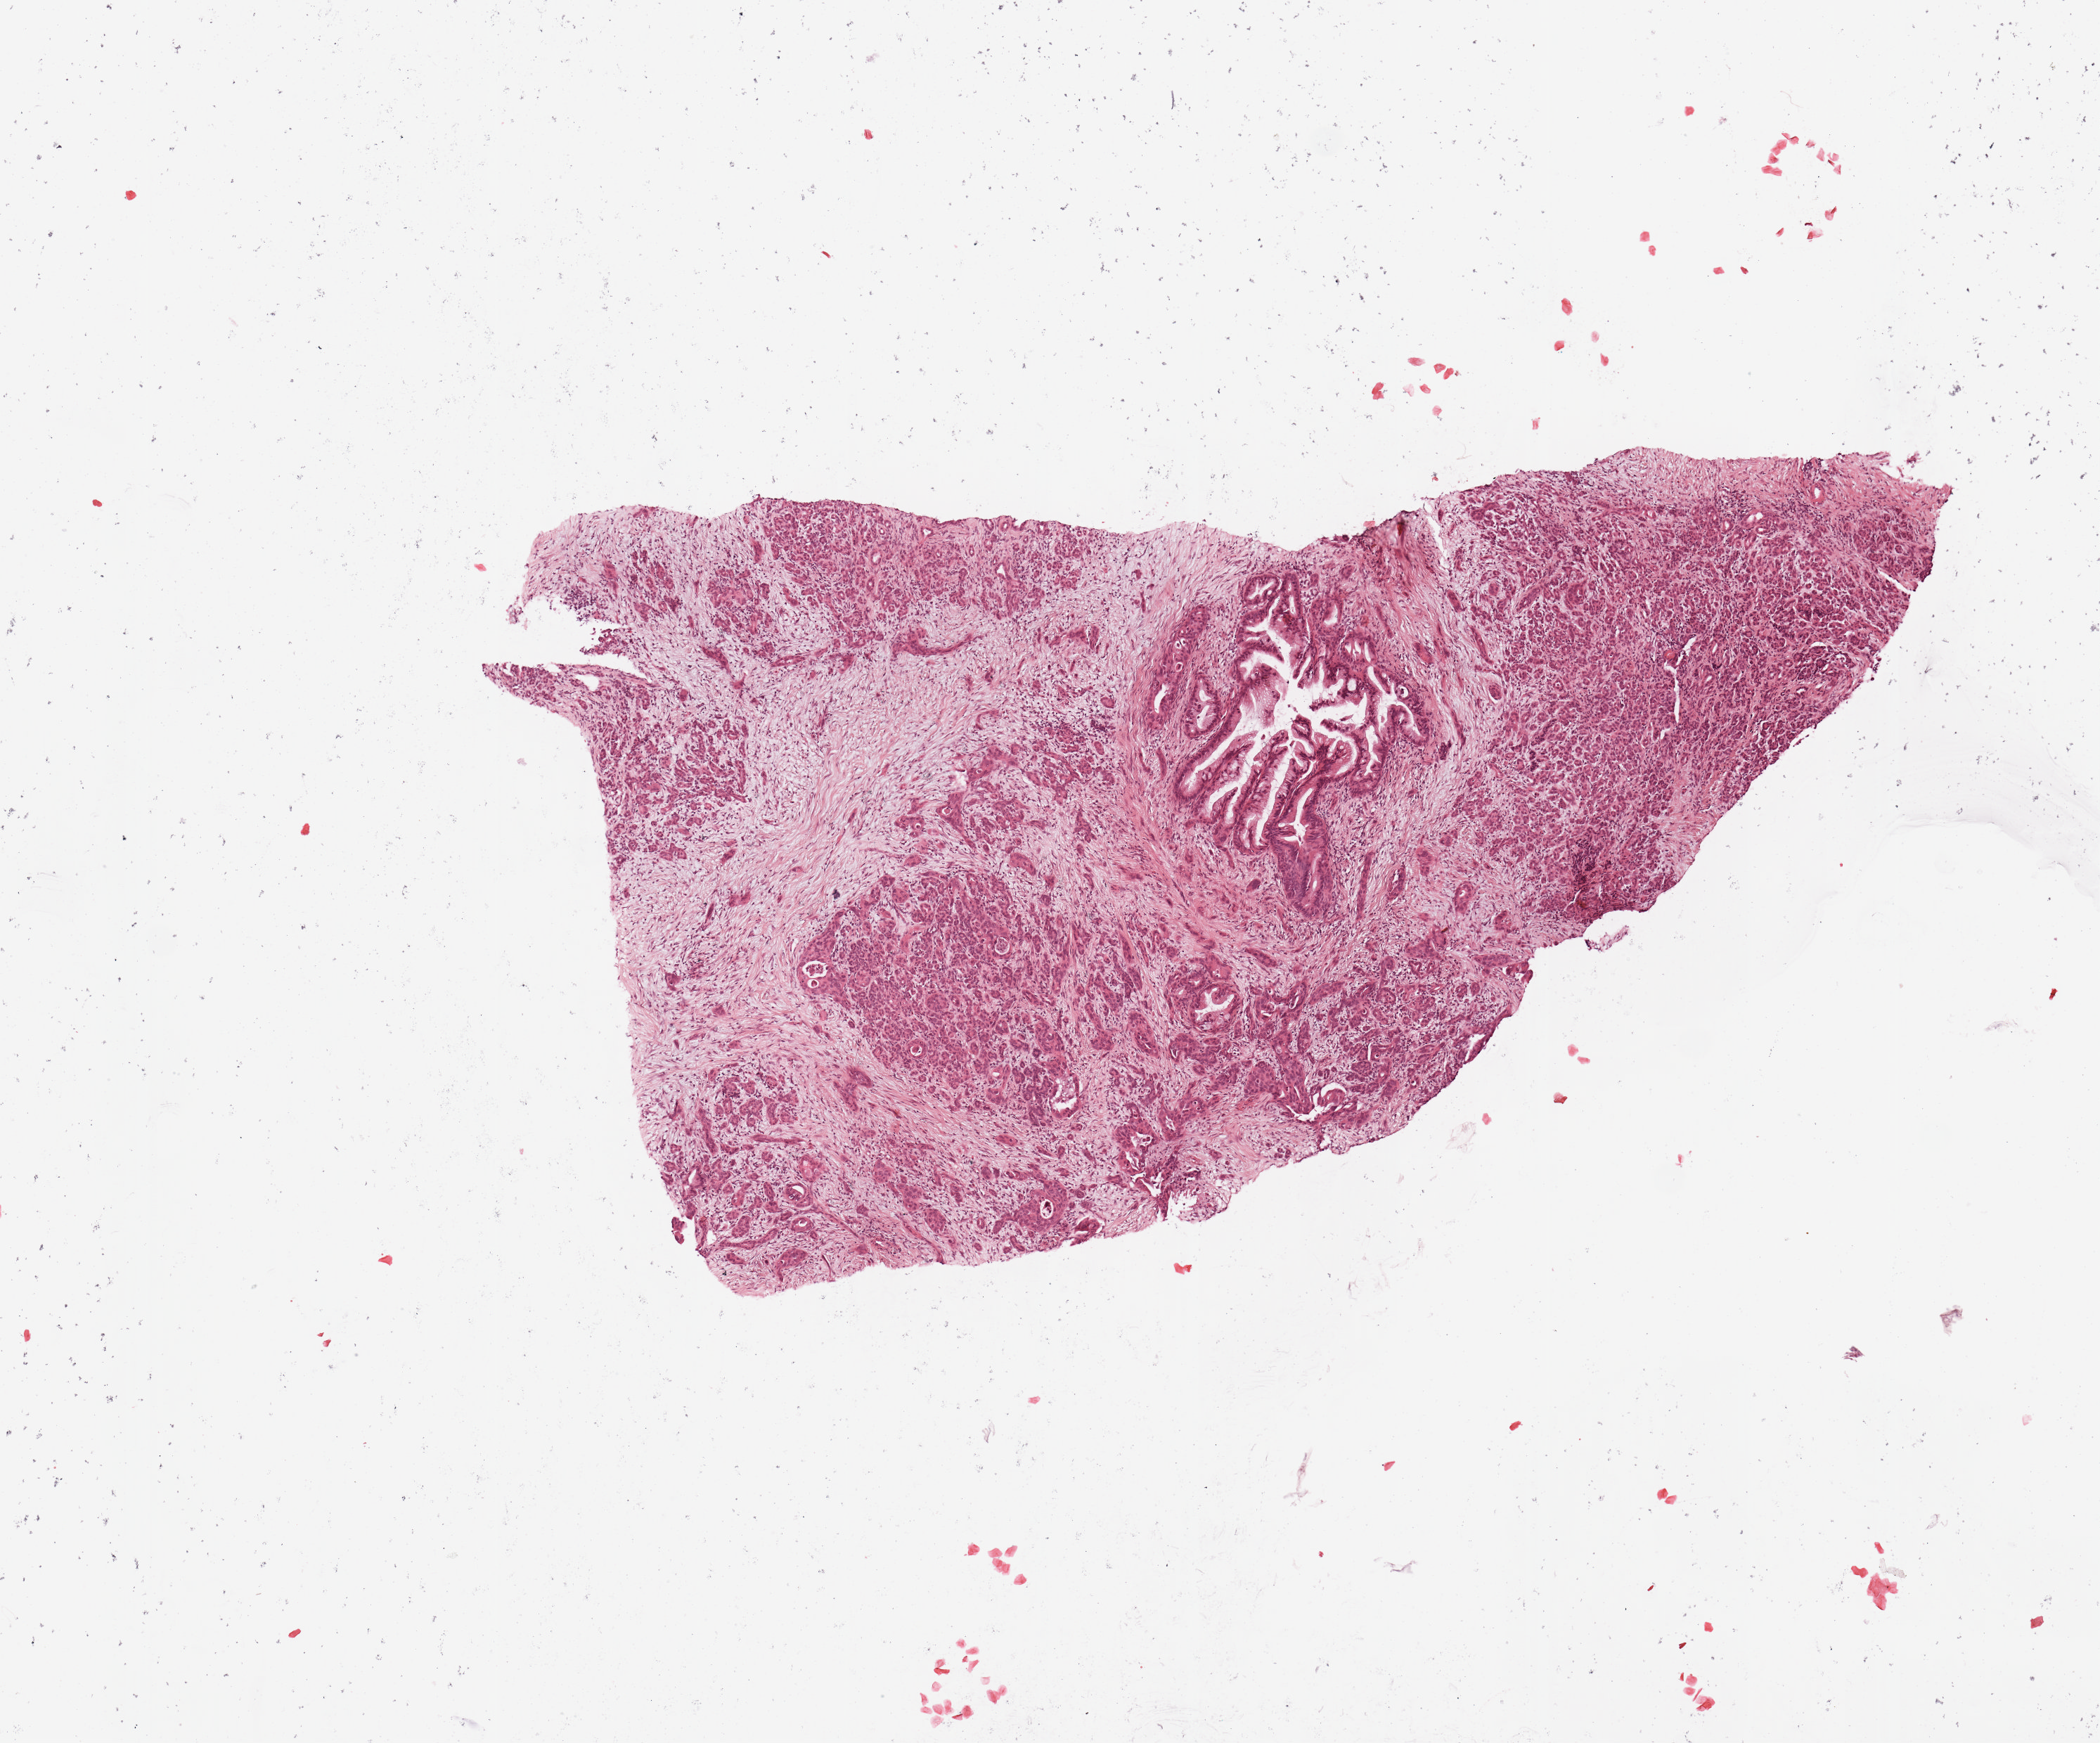
Digitized H&E-stained tissue section (whole slide), shown as a low-resolution overview of the whole scanned area (about 5.9 x 4.9 mm, from a 20x scan); tumour tissue sample, sampled site: pancreas. 63-year-old male patient. Histologic grade: G3 (poorly differentiated). Slide review estimates, as recorded: tumour nuclei 10%, necrosis 0%.
• AJCC pathologic stage: IIB
• diagnosis: Infiltrating duct carcinoma, NOS
• primary tumour site (as recorded): head